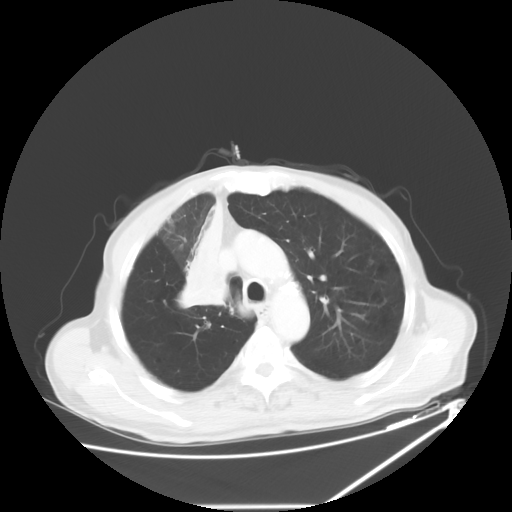
Chest CT, one axial slice. Slice 45 of 60 in the series (ordered by position). Reconstruction kernel STANDARD. Lung window (W 1500 / L -600 HU). 512 × 512 image matrix, field of view 410 × 410 mm. Male patient, age 73 years. From the clinical record (not read from this slice): clinical TNM (as recorded): T2a N1 M0.
Annotated regions visible in this slice (bounding box drawn by a radiologist):
- lung tumour (recorded histology: squamous cell carcinoma): bounding box <178,199,234,314> (left, top, right, bottom; pixels)